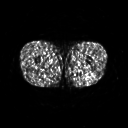
FDG PET of an extremity soft-tissue mass (from a PET/CT study), one axial slice; position 225 of 267 along the scan axis; 128 × 128 image matrix. Patient: male, 27 years. From the clinical record (not read from this slice): histological type: extraskeletal osteosarcoma; grade: high; site of the primary tumour: left adductur.
Outlined on this slice (expert contour drawn on MRI and transferred to this co-registered scan by the dataset authors):
- gross tumour volume (mass): bounding box <70,61,92,76> (left, top, right, bottom; pixels)